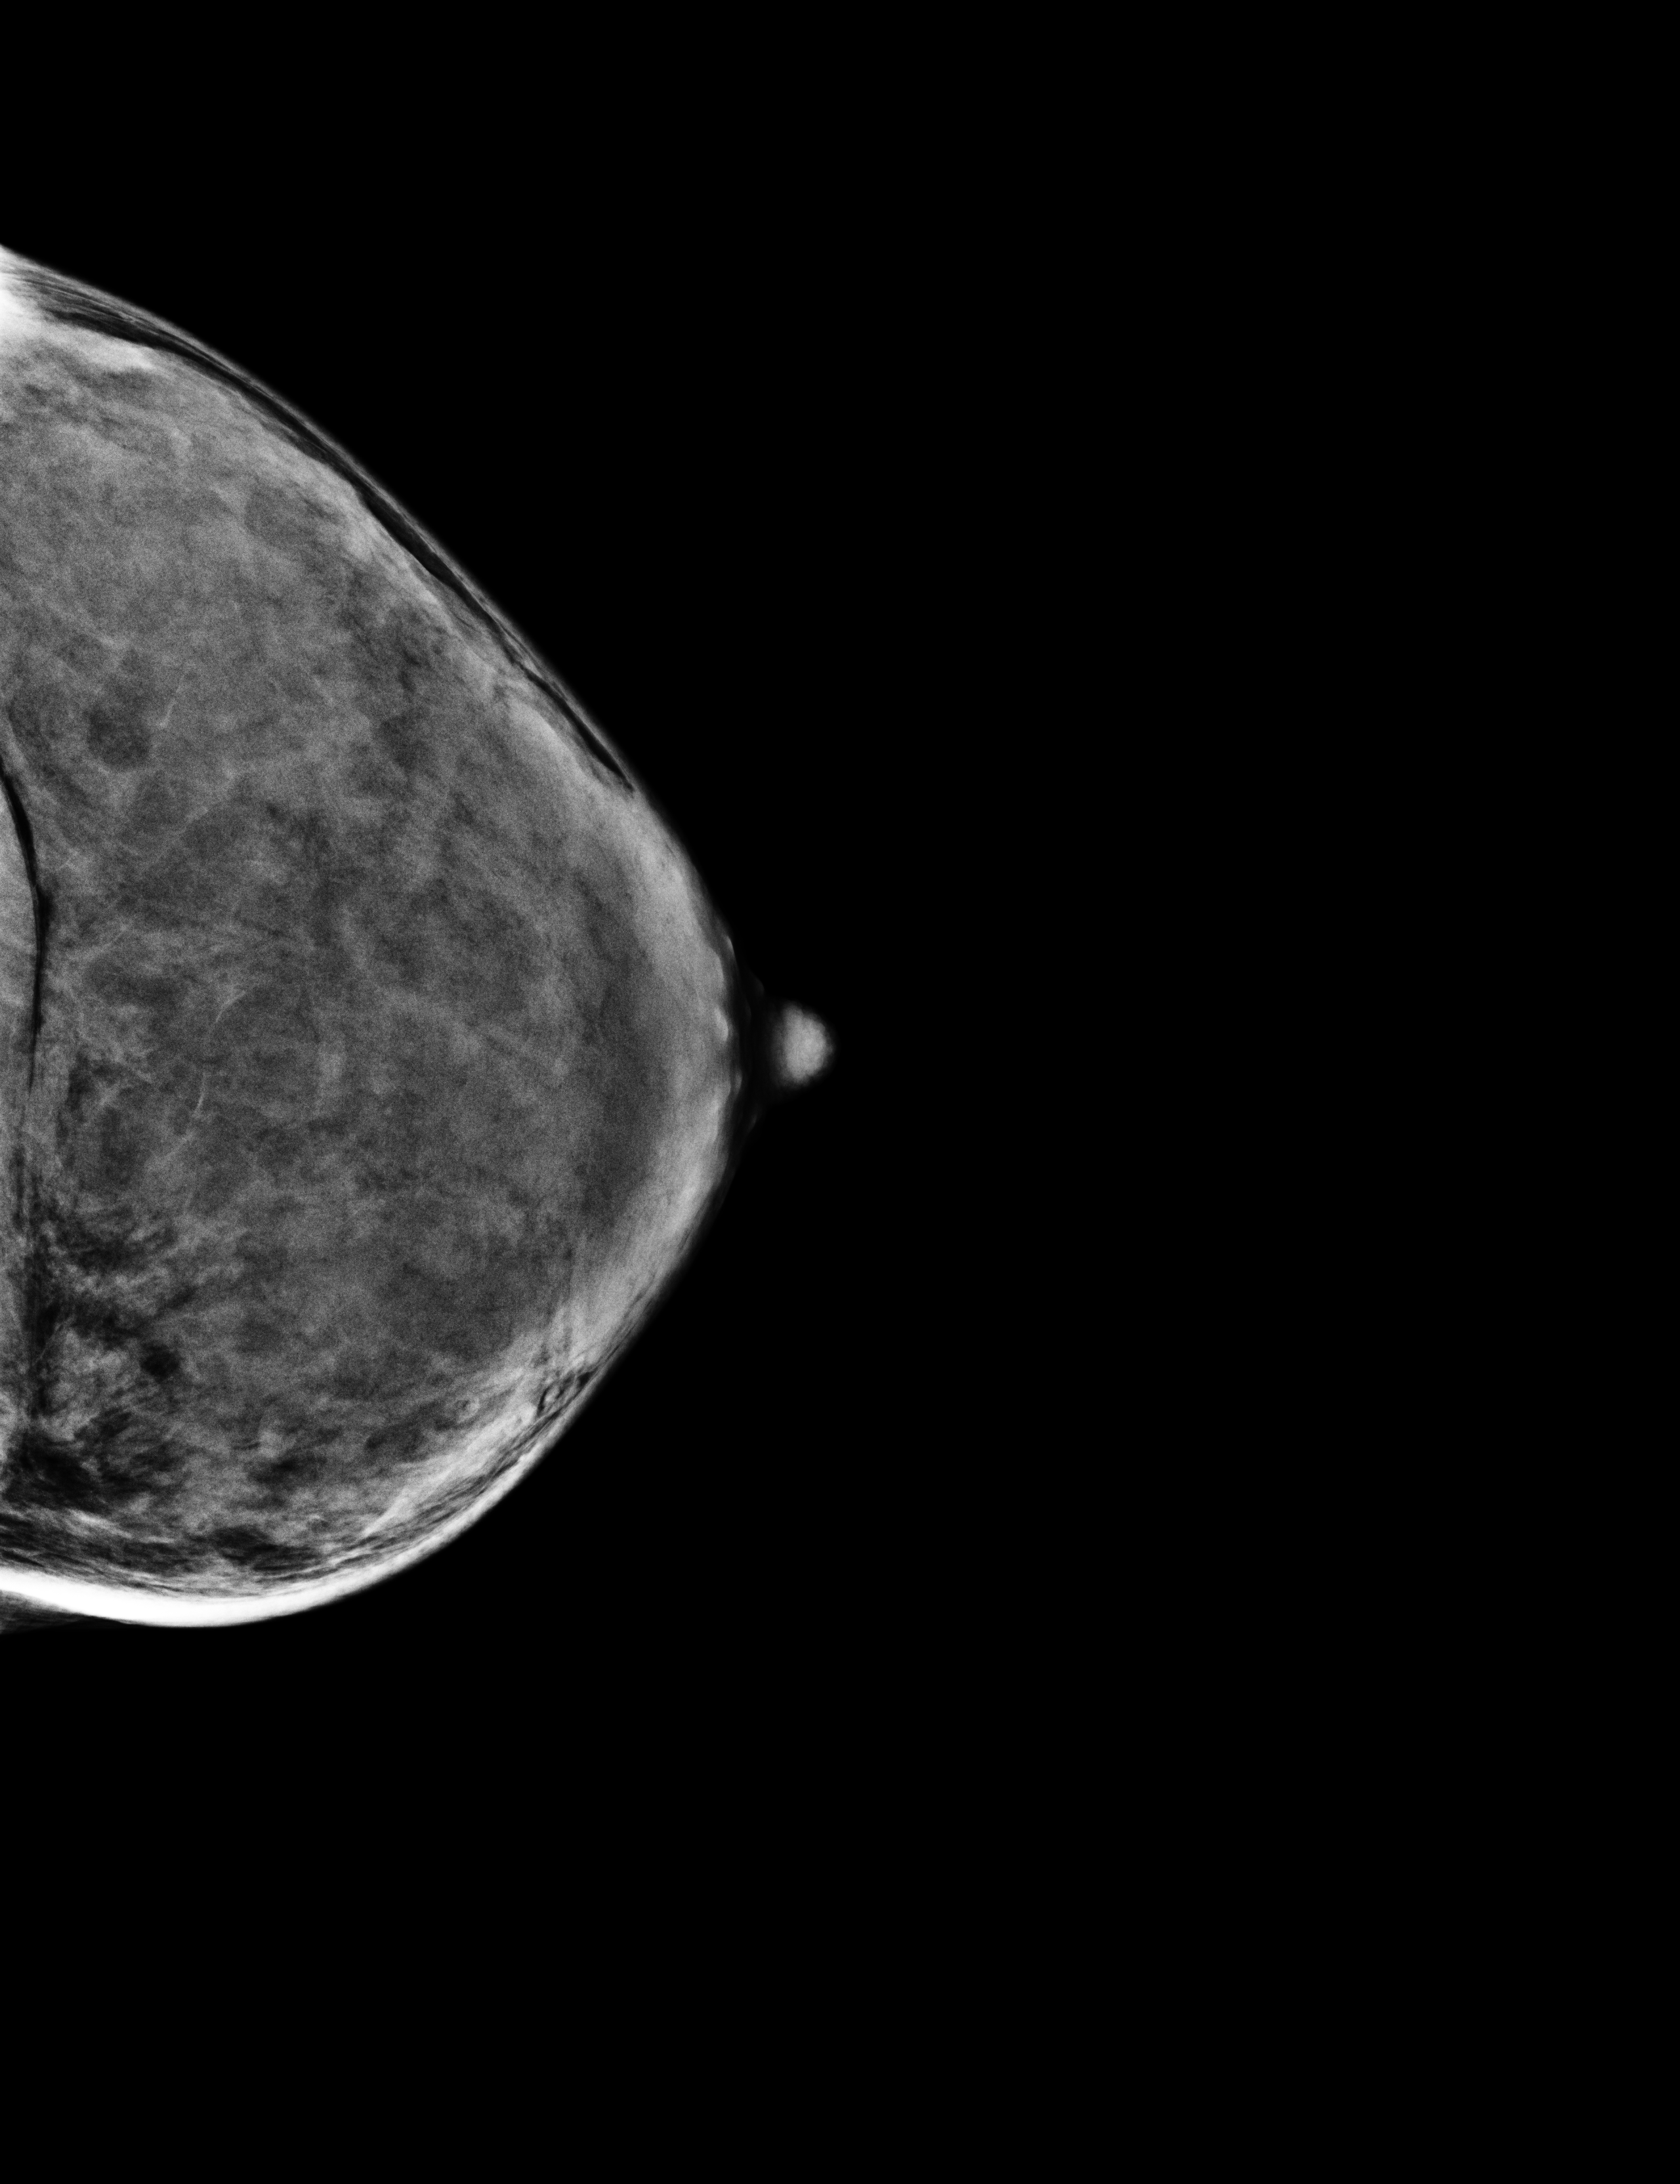
Full-field digital mammogram (FFDM), left breast, cranio-caudal projection, annual screening mammography examination, compressed breast thickness 36 mm. Patient aged 54 years (female).
- breast density at the screening exam (both breasts): extremely dense (BI-RADS density category d)
- final BI-RADS assessment for this screening round (tomosynthesis exam, both breasts): category 1
- recall: no recall after this screen